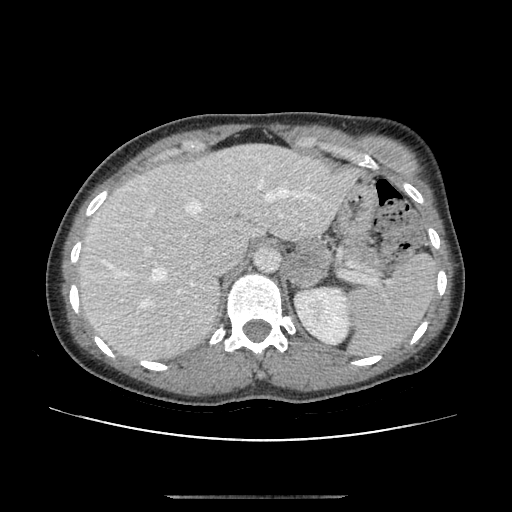
Contrast-enhanced abdominal CT, one axial slice; slice 77 of 179 in the series (ordered by position); 120 kVp; soft-tissue window (W 400 / L 40 HU); 512 × 512 image matrix. Patient: female, 51 years. Case-level facts recorded for this patient, not image findings: diagnosis: adrenocortical carcinoma; tumour side: left adrenal; tumour size at pathology: 3.5 cm; Ki-67 index: 45 %; stage (as recorded): 1.
Annotated regions visible in this slice (semi-automatically segmented with operator editing):
- mass: bounding box (x1, y1, x2, y2) in pixels: (284, 242, 331, 285)